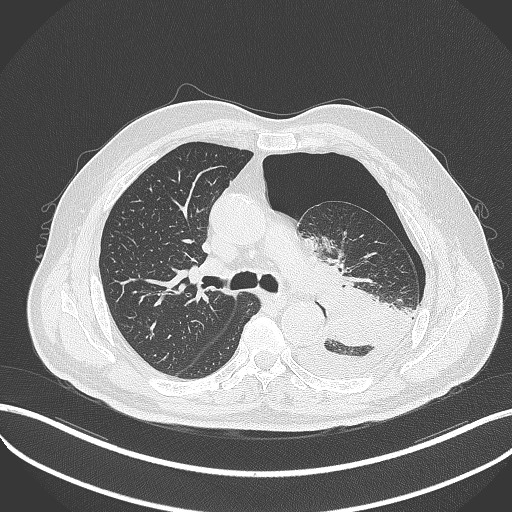
Chest CT, one axial slice; slice 331 of 464 in the series (ordered by position); lung window (W 1500 / L -600 HU); 1 mm slice thickness; 512 × 512 image matrix, field of view 400 × 400 mm. Patient: male, 76 years. From the clinical record (not read from this slice): clinical TNM (as recorded): T3 N0 M1b.
Outlined on this slice (bounding box drawn by a radiologist):
- lung tumour (recorded histology: adenocarcinoma): bounding box <319,280,398,349> (left, top, right, bottom; pixels)